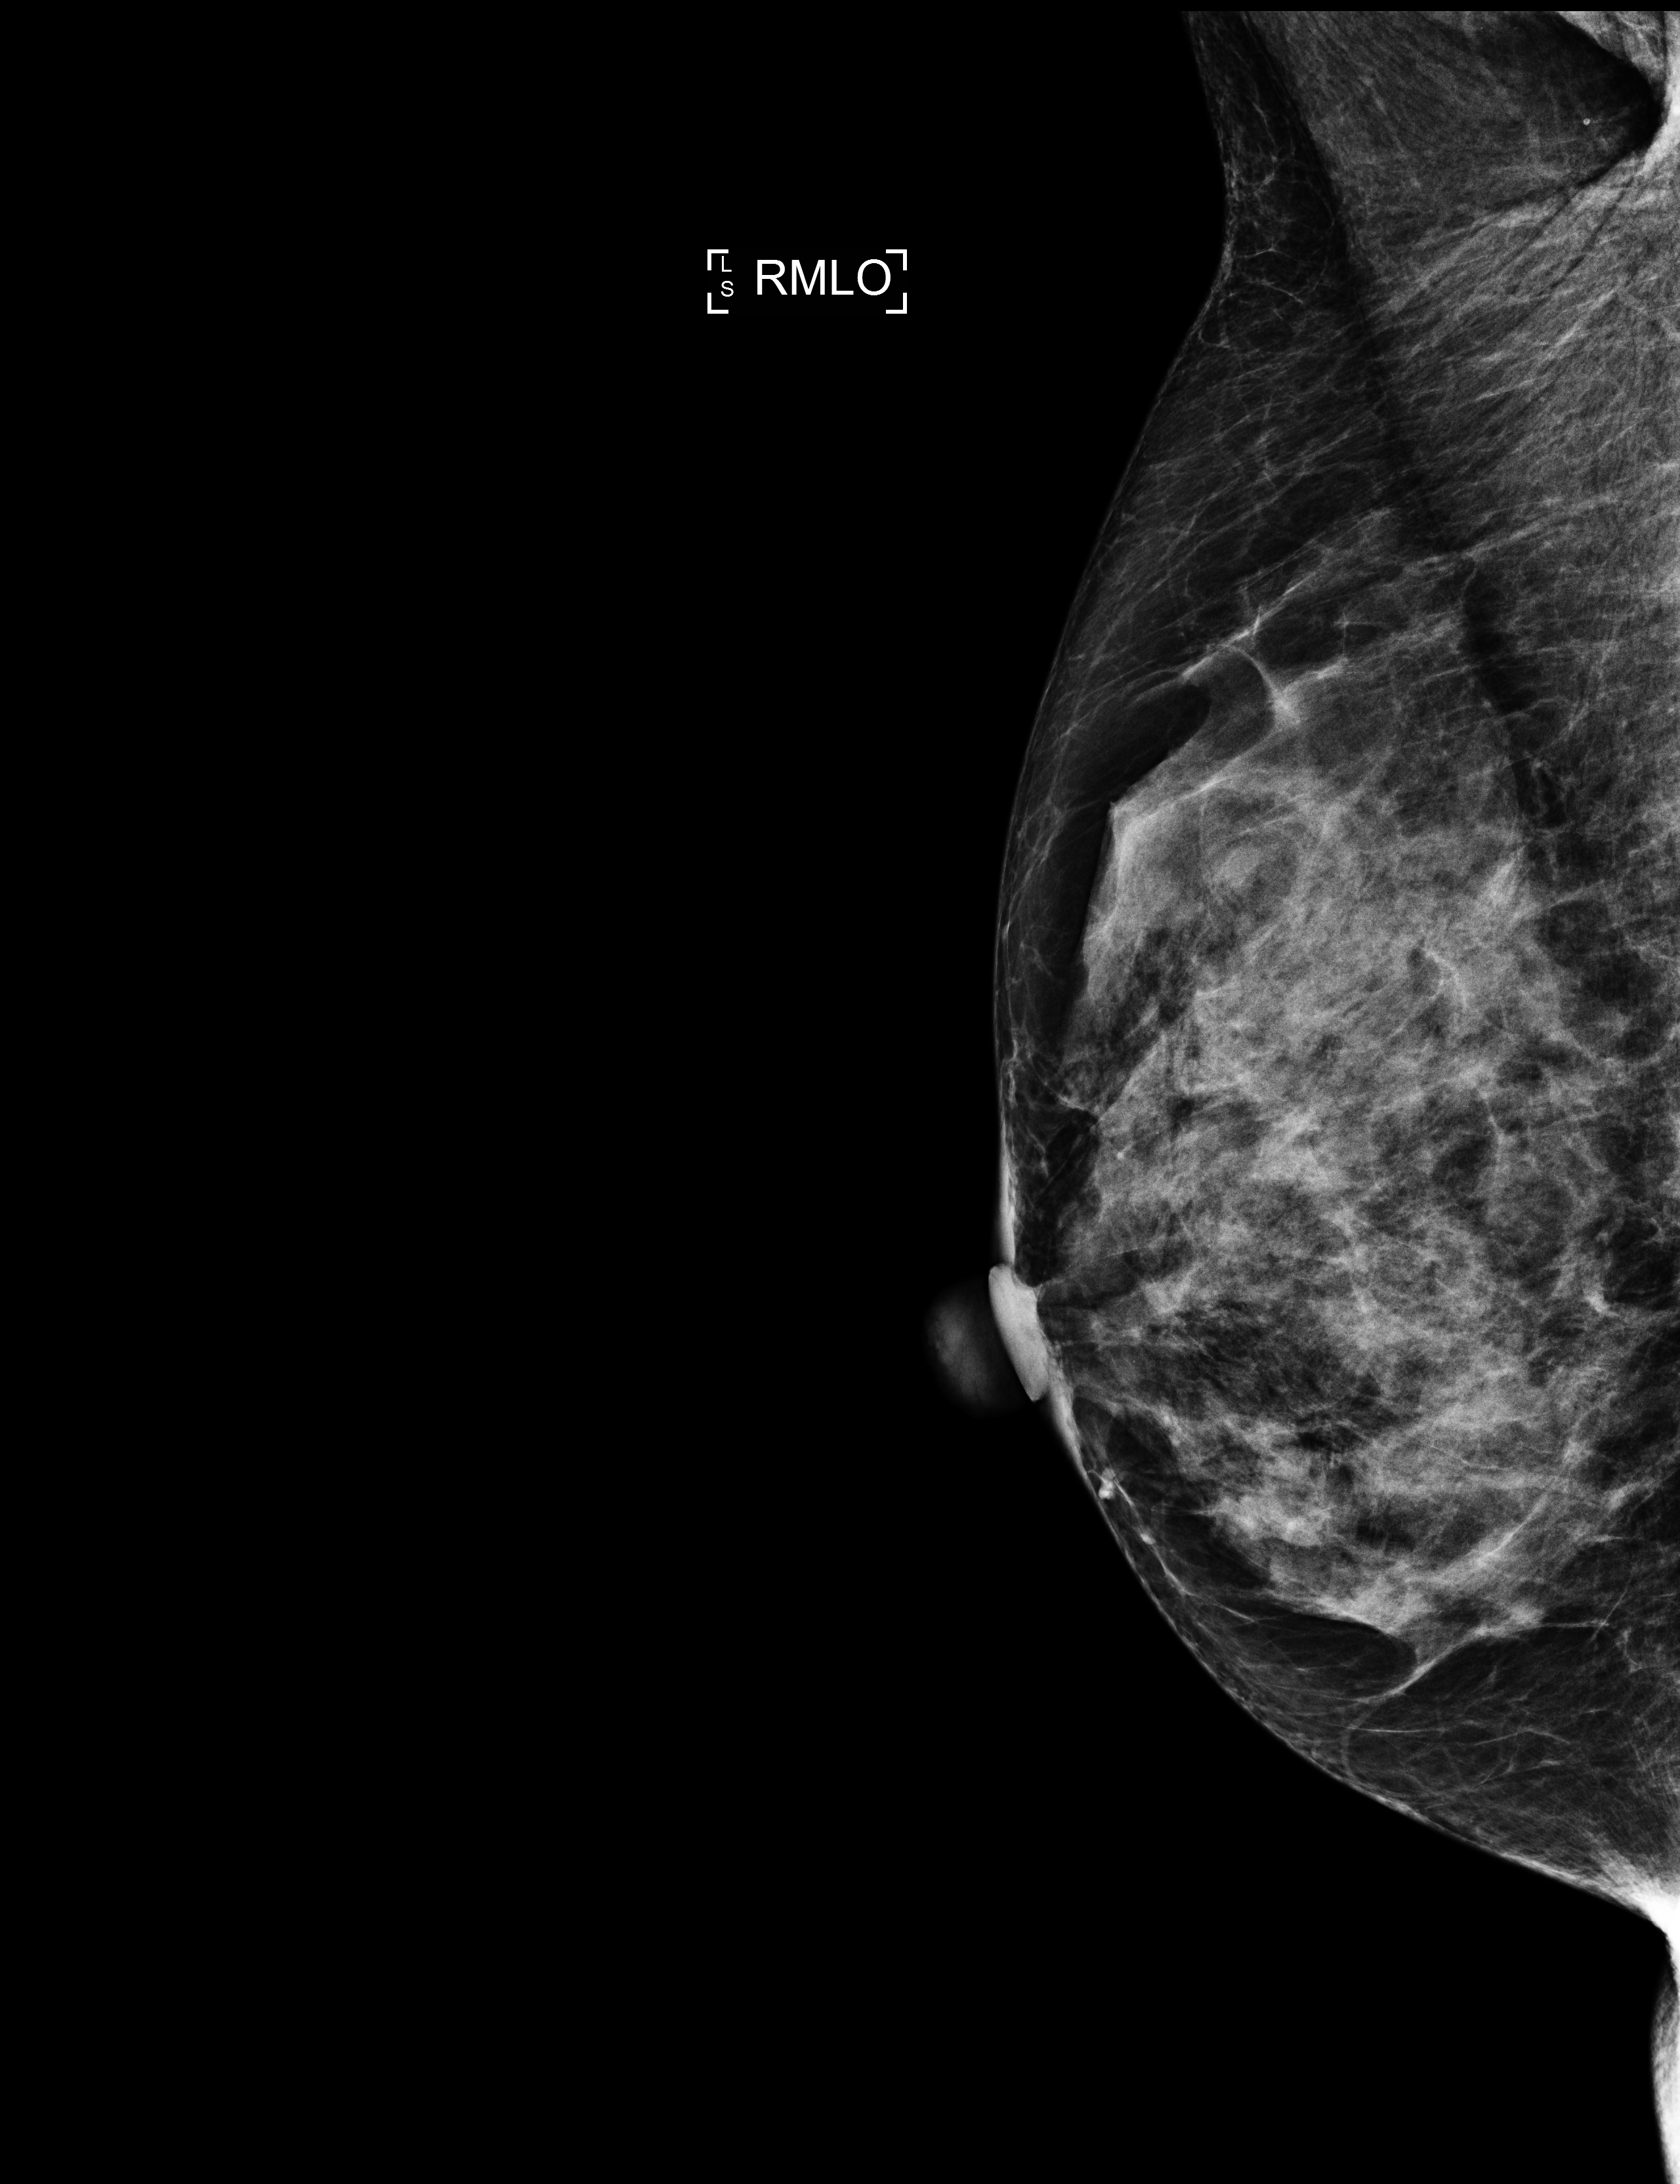
Screening examination. Patient: female, 67 years.
Image type: full-field digital mammogram. Breast: right. Projection: mediolateral oblique (MLO) view. BI-RADS breast density category at the screening exam (both breasts, scale 1–4): 4. Final BI-RADS assessment for this screening round (tomosynthesis exam, both breasts): category 2. Recall: no recall after this screen.